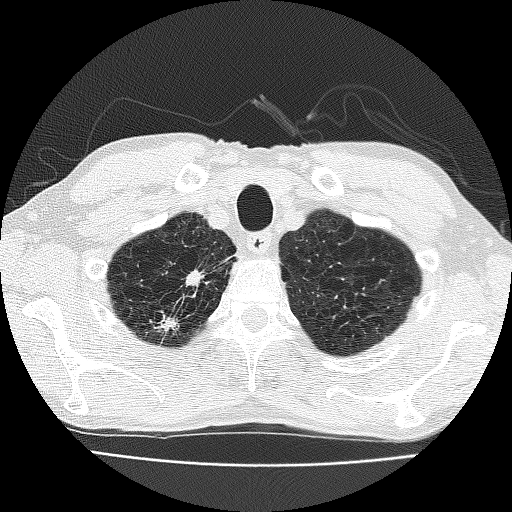
Chest CT (low-dose screening protocol), one axial image; third screening round (two years after baseline); lung window (W 1500 / L -600 HU); 2 mm slice thickness; 512 × 512 image matrix. Male participant, aged 63 years at enrolment. Current smoker at enrolment.
Expert reader's lesion annotation, box from (x=143, y=256) to (x=223, y=338) px. Screening reader's record for this exam (one nodule recorded; not confirmed to be the boxed lesion): non-calcified nodule or mass ≥4 mm, right upper lobe, 17 × 10 mm, spiculated (stellate) margins, soft tissue attenuation, pre-existing on the prior screen: yes; interval growth: yes. Participant outcome: lung cancer diagnosed 28 days after this screen — adenocarcinoma, NOS, right upper lobe, moderately differentiated (G2), stage IIIB (AJCC 6th edition), 17 mm at pathology.